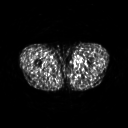
FDG PET of an extremity soft-tissue mass (from a PET/CT study), one axial slice; 3.27 mm slice thickness; 128 × 128 image matrix. Male patient, age 29 years. From the clinical record (not read from this slice): histological type: mixoid liposarcoma; grade: low; site of the primary tumour: left thigh.
Annotated regions visible in this slice (expert contour drawn on MRI and transferred to this co-registered scan by the dataset authors):
- gross tumour volume (mass): box from (x=72, y=55) to (x=82, y=65) px